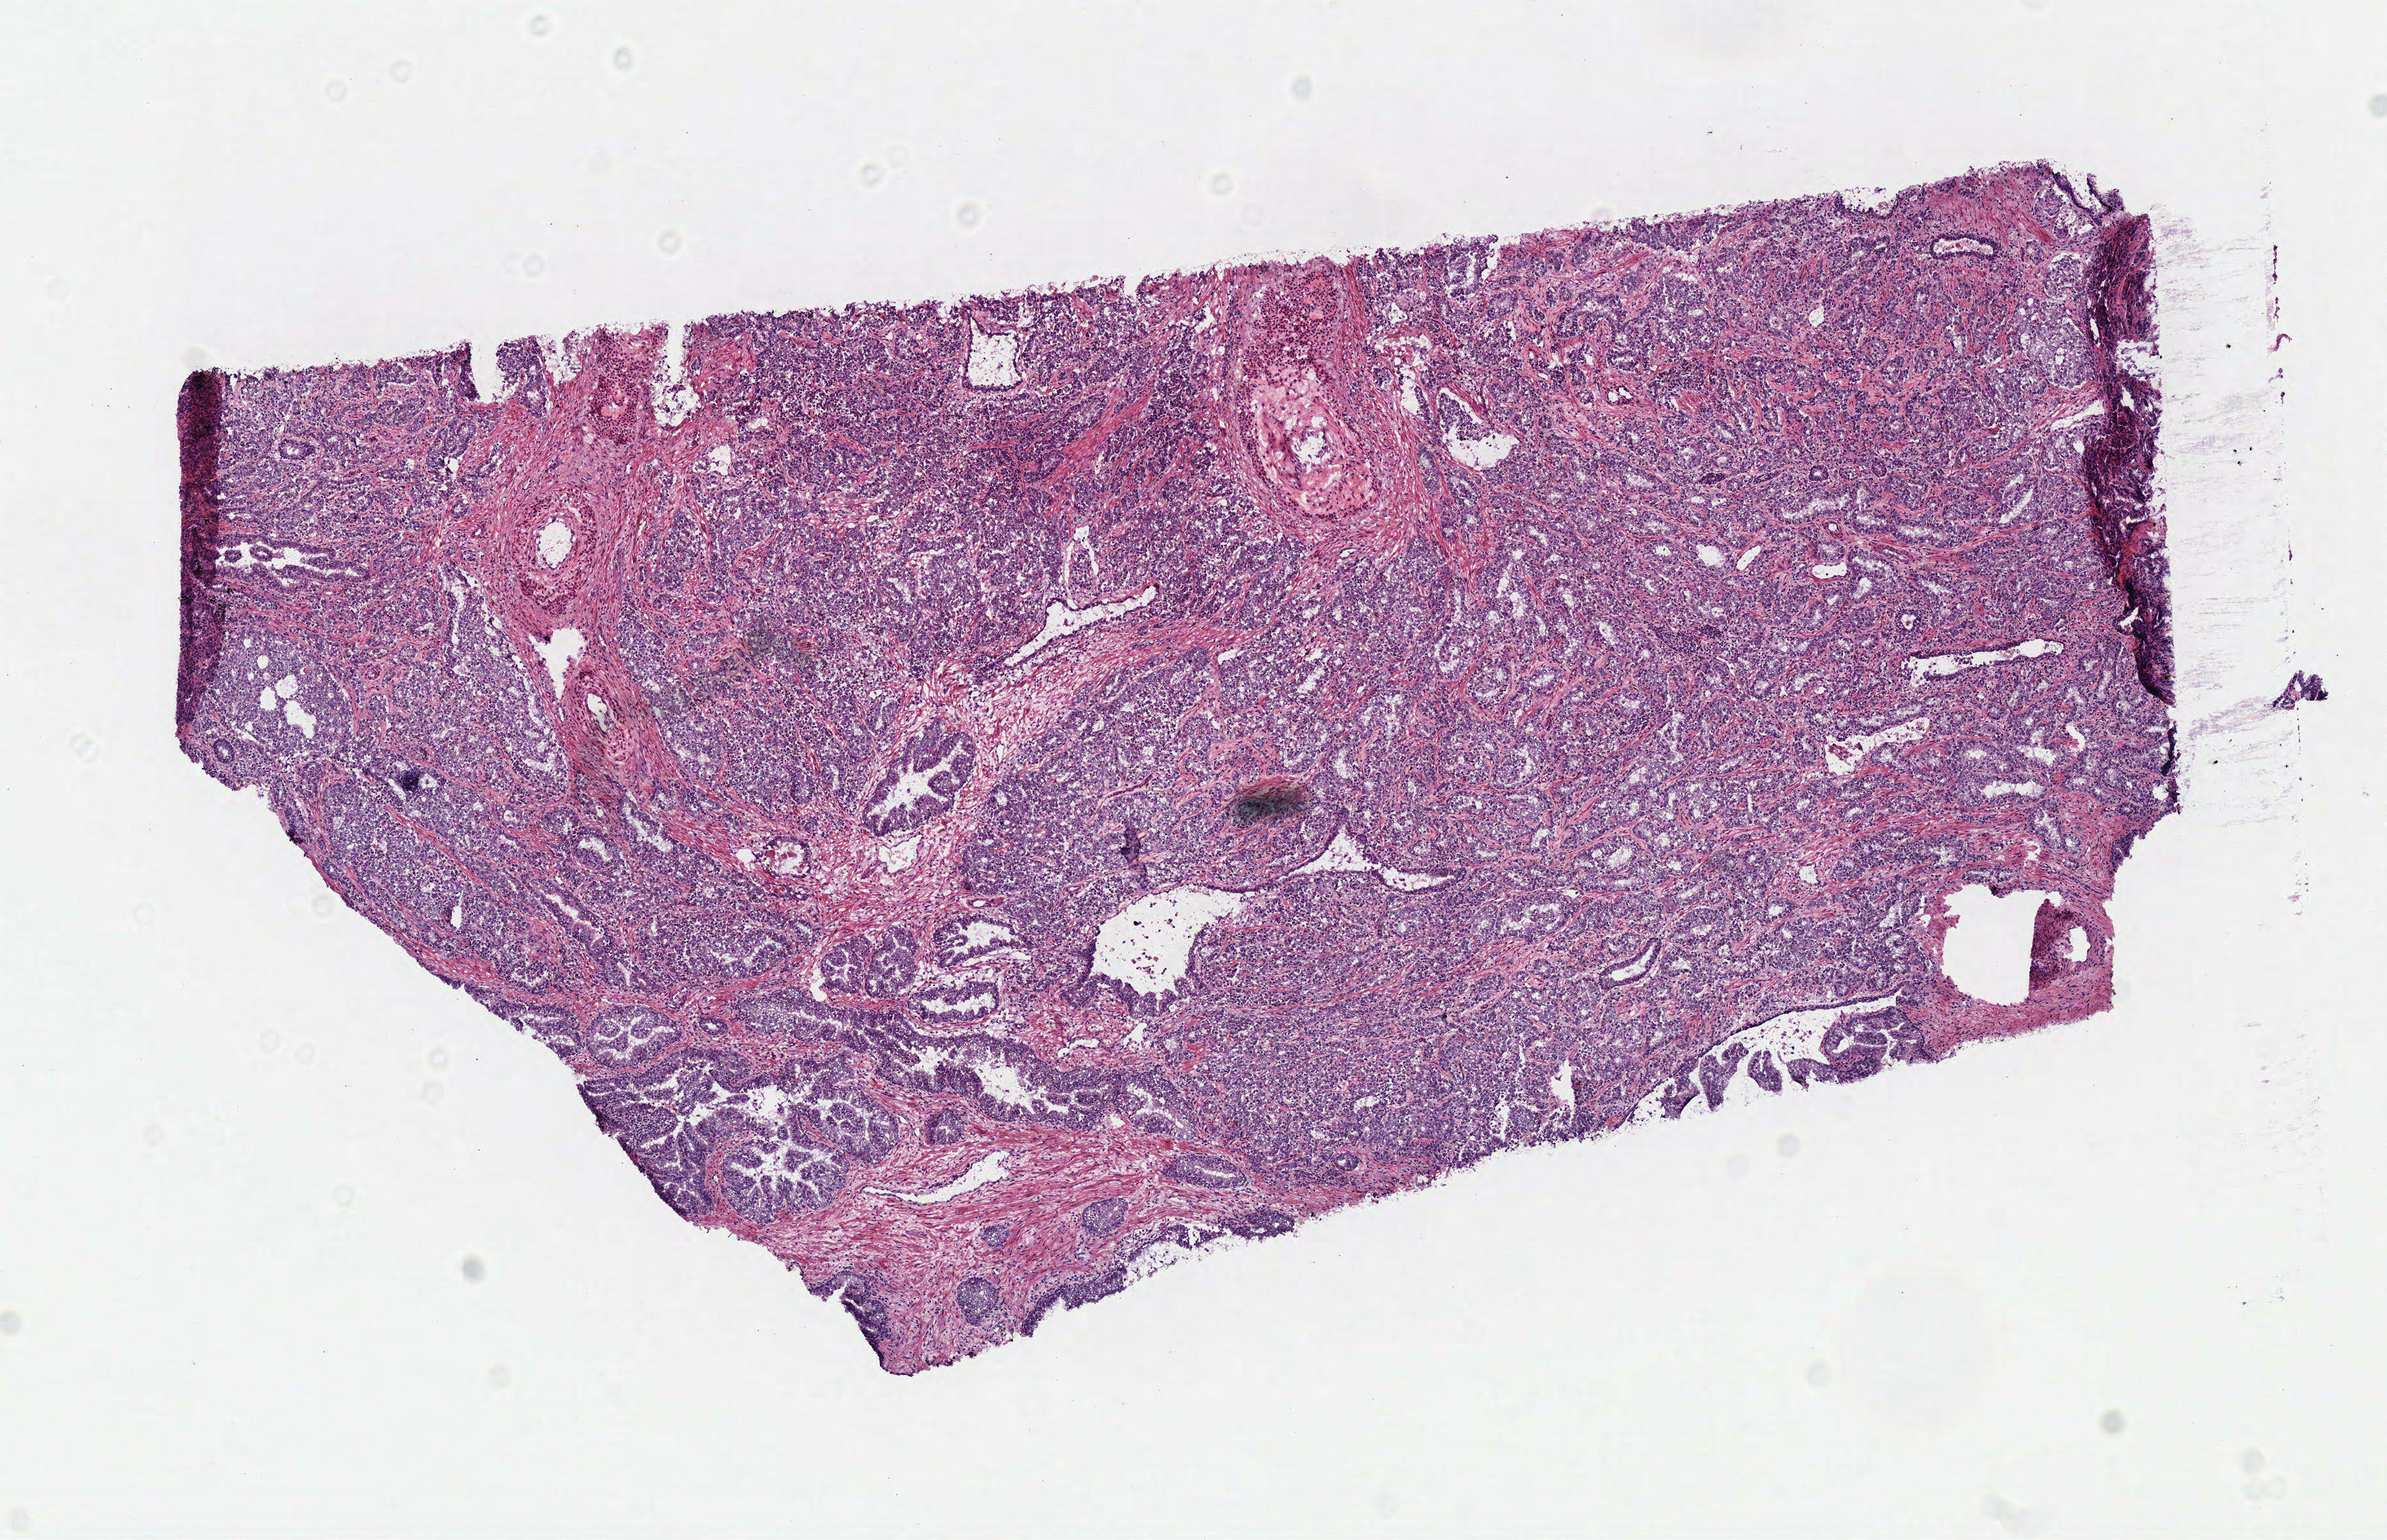
Whole-slide histology image, H&E, a low-resolution overview of the entire scanned area, about 7.3 x 4.7 mm (from a 40x scan). Frozen section from the top of the tissue portion. Prostate, primary tumour sample. Male patient; age at initial diagnosis 69 years. Gleason score: 7 (3+4). Pathologist review of this section (percent, as recorded): tumour cells 85%, tumour nuclei 85%, normal cells 10%, stromal cells 5%, necrosis 0%.
Lymph nodes positive (case pathology): 0 of 3 examined. Pathologic diagnosis: Acinar cell carcinoma.